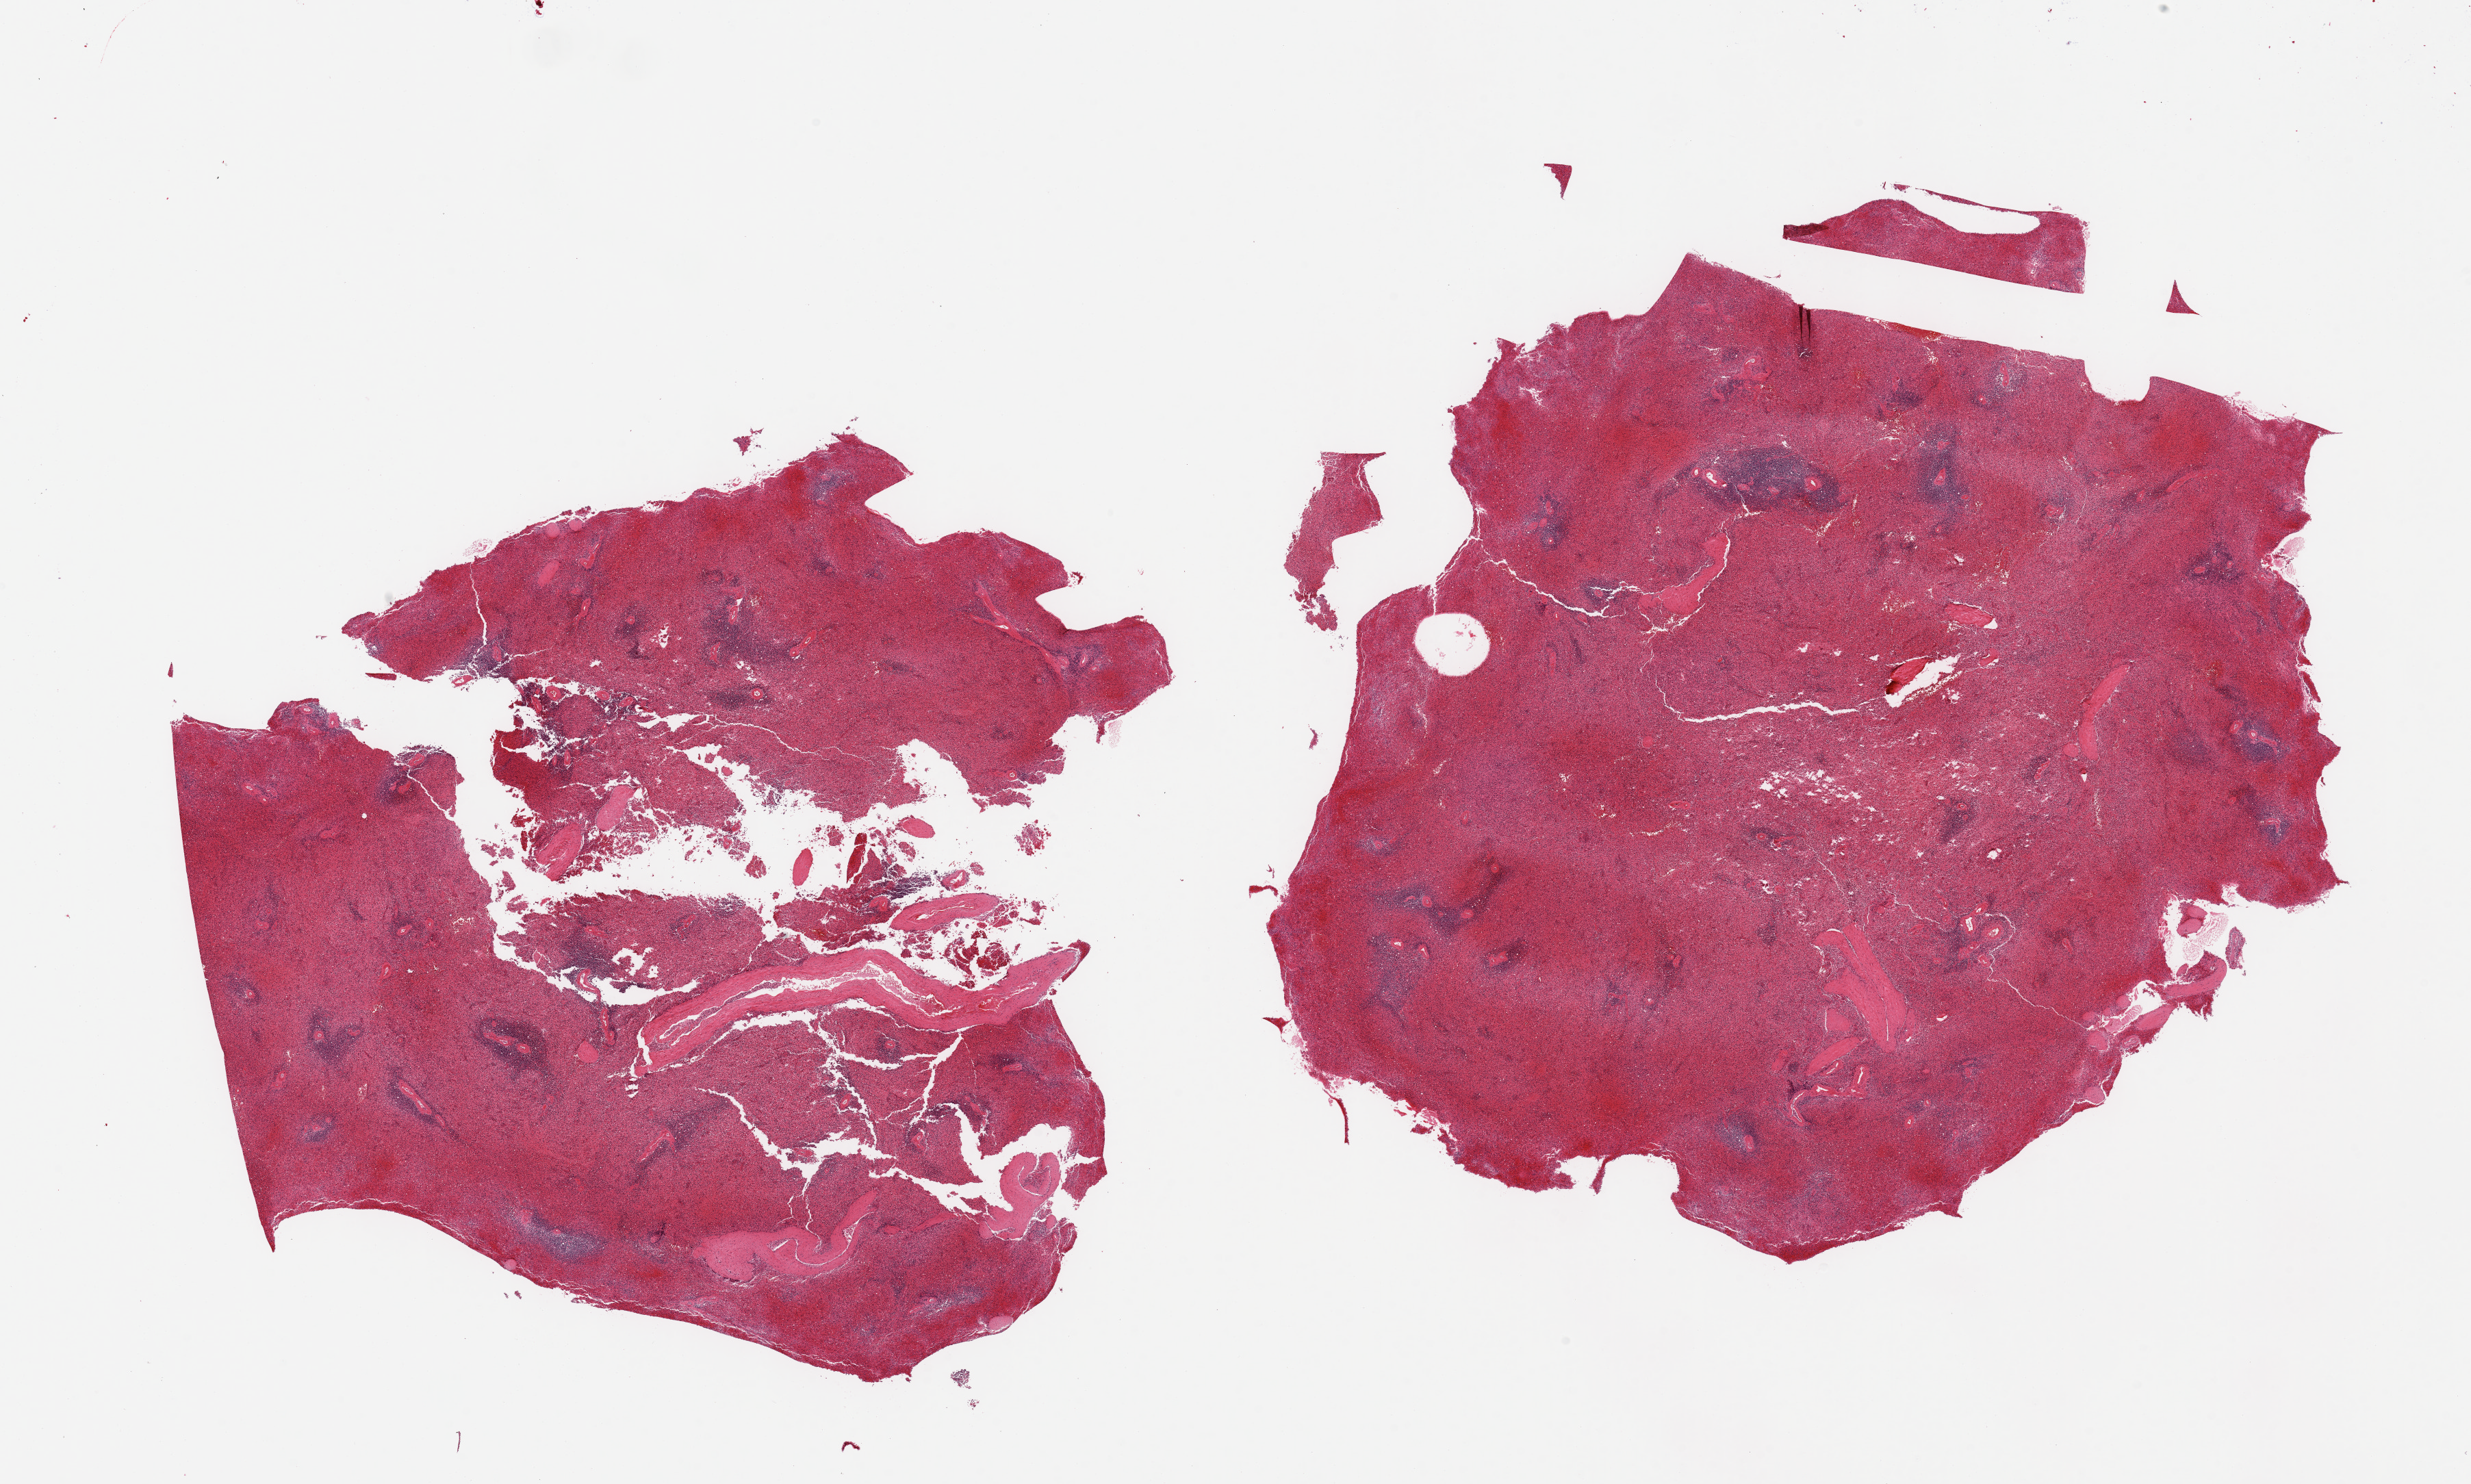
Digitized H&E-stained section — whole scanned area (about 28.5 x 17.1 mm) shown as a low-resolution overview. PAXgene-fixed paraffin-embedded (PFPE) section. Target tissue: spleen. Tissue donor sample. Male donor.
Reviewer comment on this tissue sample: 2 pieces, marked congestion.